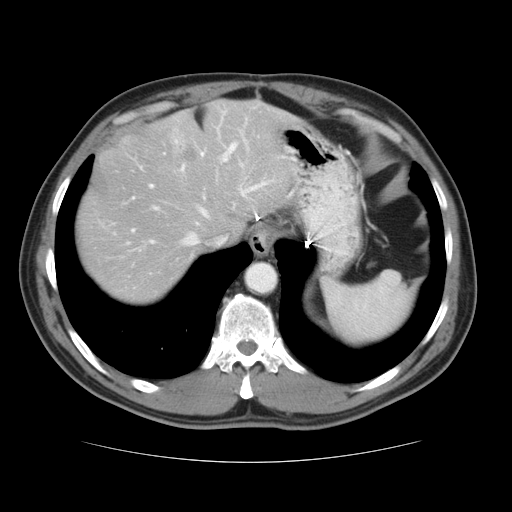
Contrast-enhanced abdominal CT, one axial slice; position 29 of 37 along the scan axis; reconstruction kernel STANDARD; 120 kVp; intravenous contrast given; soft-tissue window (W 400 / L 40 HU); 5 mm slice thickness; 512 × 512 image matrix, field of view 374 × 374 mm. Male patient, age 66 years. Case-level facts recorded for this patient, not image findings: diagnosis: colorectal cancer liver metastases, imaged before liver resection; multiple liver metastases: yes.
Outlined on this slice (outlined manually by an expert reader):
- hepatic veins: box from (x=128, y=164) to (x=264, y=246) px
- liver: (x=77, y=100)–(x=301, y=304)
- planned liver remnant (the part of the liver to remain after resection): (x=77, y=106)–(x=301, y=304)
- portal vein (with intrahepatic branches): (x=131, y=142)–(x=238, y=232)
- liver metastasis: (x=176, y=141)–(x=204, y=170)